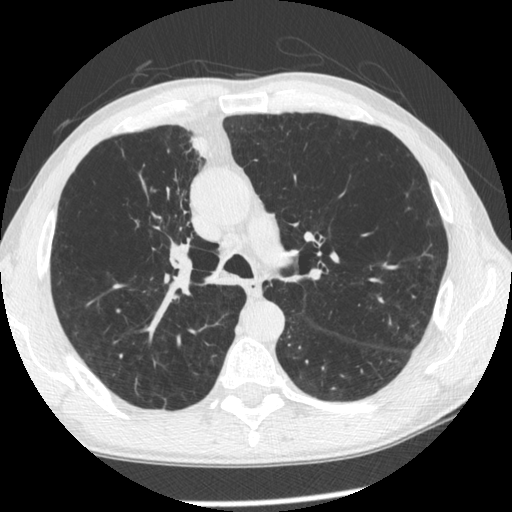
Low-dose screening chest CT, one axial slice; slice 157 of 261 in the series (ordered by position); lung window (W 1500 / L -600 HU); 1.25 mm slice thickness; 512 × 512 image matrix, field of view 340 × 340 mm.
Outlined on this slice (manually delineated by an expert):
- lesion 1 (tumor, upper lobe of right lung): bounding box (x1, y1, x2, y2) in pixels: (191, 136, 209, 158)